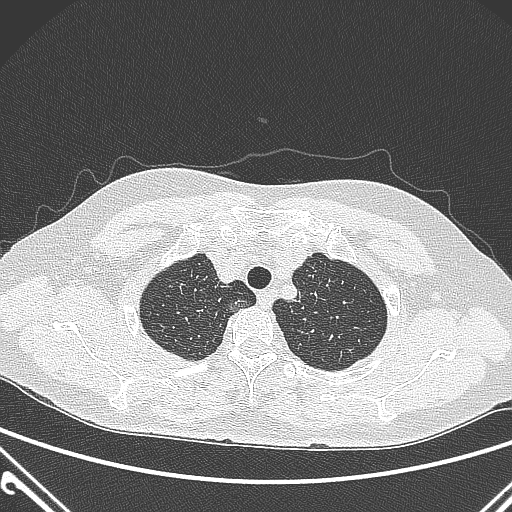
Chest CT, one axial slice. Position 244 of 300 along the scan axis. Lung window (W 1500 / L -600 HU). 1 mm slice thickness. 512 × 512 image matrix, field of view 350 × 350 mm. Female patient, age 54 years. Case-level facts recorded for this patient, not image findings: clinical TNM (as recorded): T1a N0 M0; histopathological grade: G1.
Structures marked on this image (rectangle marked by the reading radiologist):
- lung tumour (recorded histology: adenocarcinoma): bounding box [x1, y1, x2, y2] px = [224, 292, 251, 318]